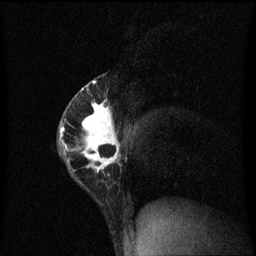
Breast MRI (dynamic contrast-enhanced), one sagittal slice; position 39 of 60 along the scan axis; dynamic contrast-enhanced series, image 2 of 3 at this slice position (ordered by acquisition); 1.5 T; TE 4.2 ms, TR 8.4 ms; 256 × 256 image matrix, field of view 200 × 200 mm. Patient: female, 40 years.
Structures marked on this image (semi-automatically segmented with operator editing):
- analysis volume of interest (the breast-tissue region the enhancement analysis was run in; not a lesion): bounding box [x1, y1, x2, y2] px = [59, 74, 122, 203]
- tumour enhancement mask (voxels above the 70 % enhancement threshold inside the analysis volume of interest): [60, 82, 121, 173]